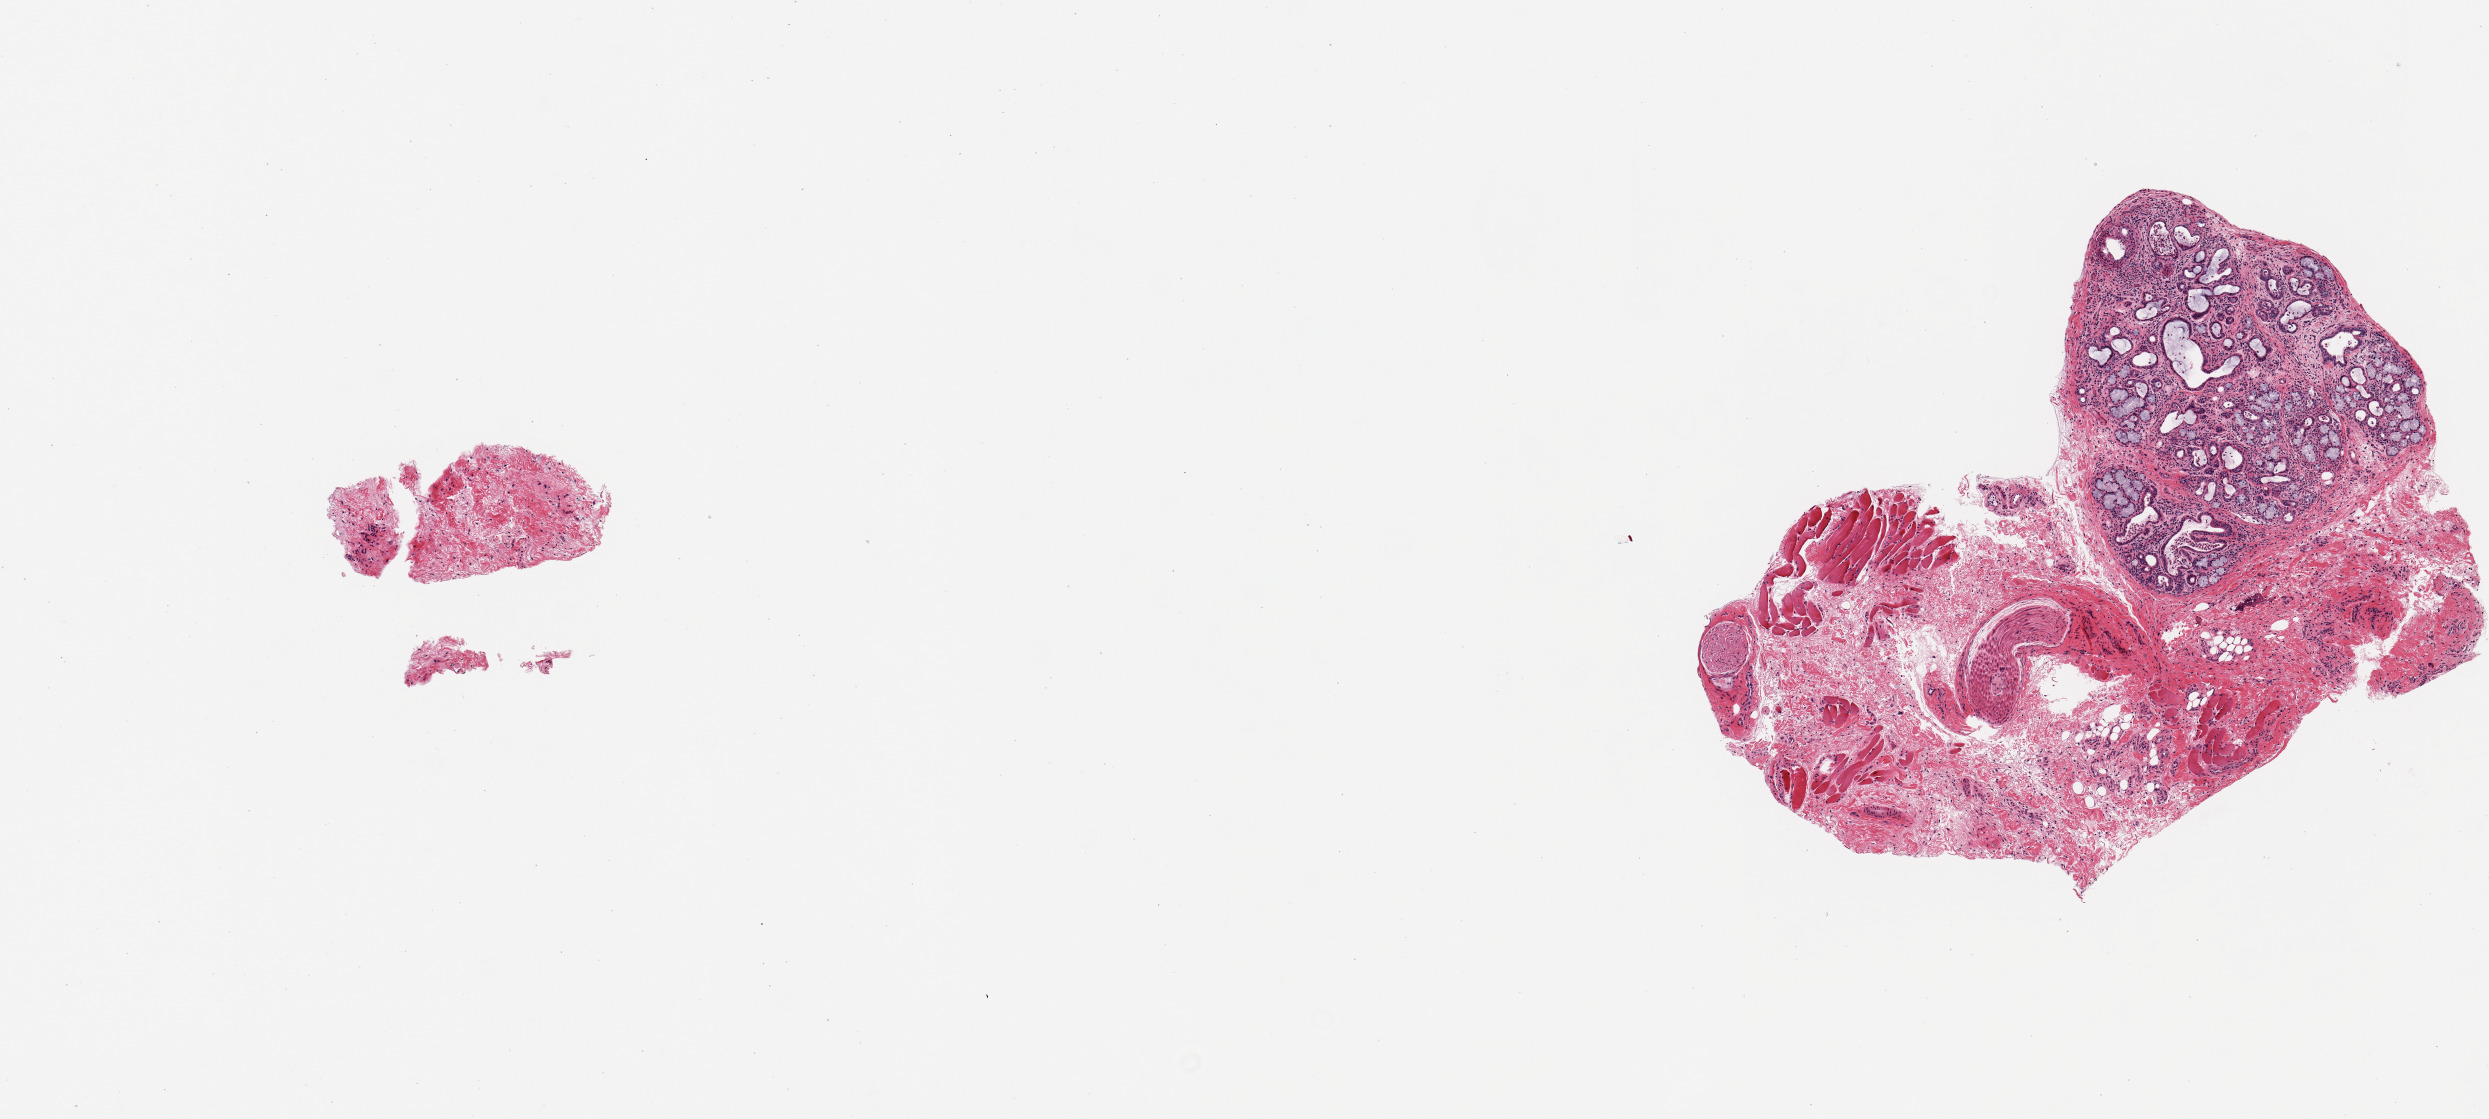
Whole-slide image, H&E stain, low-resolution overview of the scanned area, about 9.8 x 4.4 mm. PAXgene-fixed, paraffin-embedded tissue. Sampled site (target tissue): minor salivary gland. Tissue donor sample. Donor sex: male.
Review note (as recorded): 2 pieces; one represents 40% acutely inflamed salivary gland and 60% fibrovascular tissue, skeletal muscle and nerves; second represents connective tissue only (very small piece).